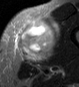
MRI of an extremity soft-tissue mass, one axial slice; position 26 of 45 along the scan axis; STIR; MR volume resampled by the dataset authors to the PET/CT grid (not the native acquisition matrix); 3.27 mm slice thickness; 79 × 87 image matrix. Male patient. From the clinical record (not read from this slice): histological type: pleiomorphic leiomyosarcoma; grade: high; site of the primary tumour: left thigh.
Annotated regions visible in this slice (expert contour drawn on MRI and transferred to this co-registered scan by the dataset authors):
- gross tumour volume including surrounding oedema: box from (x=16, y=18) to (x=60, y=63) px
- gross tumour volume (mass): (x=18, y=20)–(x=55, y=62)